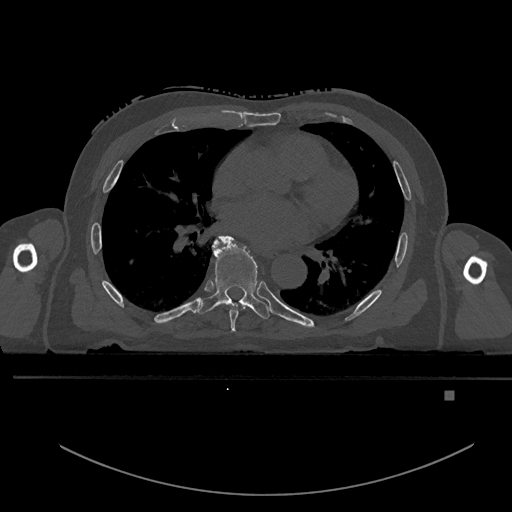
CT including the spine, one axial slice. Slice 271 of 969 in the series (ordered by position). Bone window (W 1800 / L 400 HU). 0.5 mm slice thickness. 512 × 512 image matrix, field of view 456 × 456 mm. Patient: male, 82 years. Case-level facts recorded for this patient, not image findings: primary cancer: prostate; vertebrae with lytic lesions (as recorded): T11, T9, T8, T2.
Annotated regions visible in this slice (semi-automatically segmented with operator editing):
- T6 vertebra: box from (x=229, y=302) to (x=247, y=332) px
- T7 vertebra: (x=198, y=235)–(x=270, y=319)